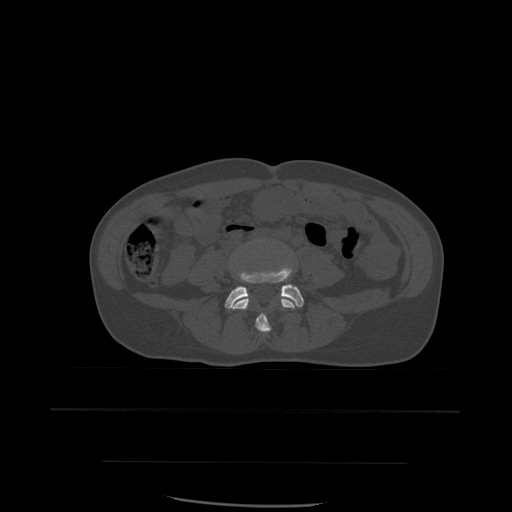
CT including the spine, one axial slice. Slice 159 of 574 in the series (ordered by position). Bone window (W 1800 / L 400 HU). 1.25 mm slice thickness. 512 × 512 image matrix. Patient age 48 years. From the clinical record (not read from this slice): primary cancer: lung.
Structures marked on this image (semi-automatically segmented with operator editing):
- L4 vertebra: bounding box (x1, y1, x2, y2) in pixels: (231, 249, 297, 334)
- L5 vertebra: (225, 268, 304, 309)